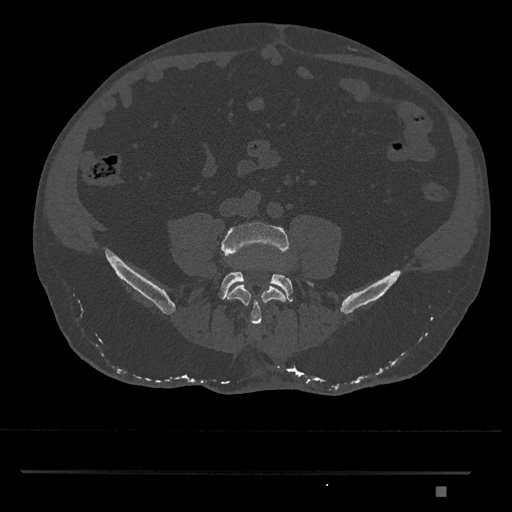
CT including the spine, one axial slice. Position 585 of 1134 along the scan axis. Reconstruction kernel Br40s/3. 120 kVp. Bone window (W 1800 / L 400 HU). 0.5 mm slice thickness. 512 × 512 image matrix, field of view 429 × 429 mm. Male patient, age 65 years. From the clinical record (not read from this slice): primary cancer: prostate.
Annotated regions visible in this slice (semi-automatic segmentation, software-assisted and operator-edited):
- L4 vertebra: box from (x=220, y=222) to (x=291, y=325) px
- L5 vertebra: (x=218, y=270)–(x=315, y=302)